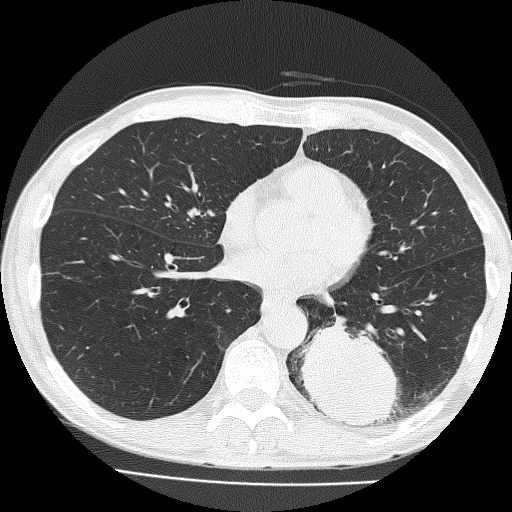
Low-dose screening chest CT, one axial slice. Position 70 of 160 along the scan axis. 120 kVp. Lung window (W 1500 / L -600 HU). 2 mm slice thickness. 512 × 512 image matrix.
Structures marked on this image (manually delineated by an expert):
- lesion 1 (tumor, lower lobe of left lung): box from (x=301, y=318) to (x=399, y=427) px